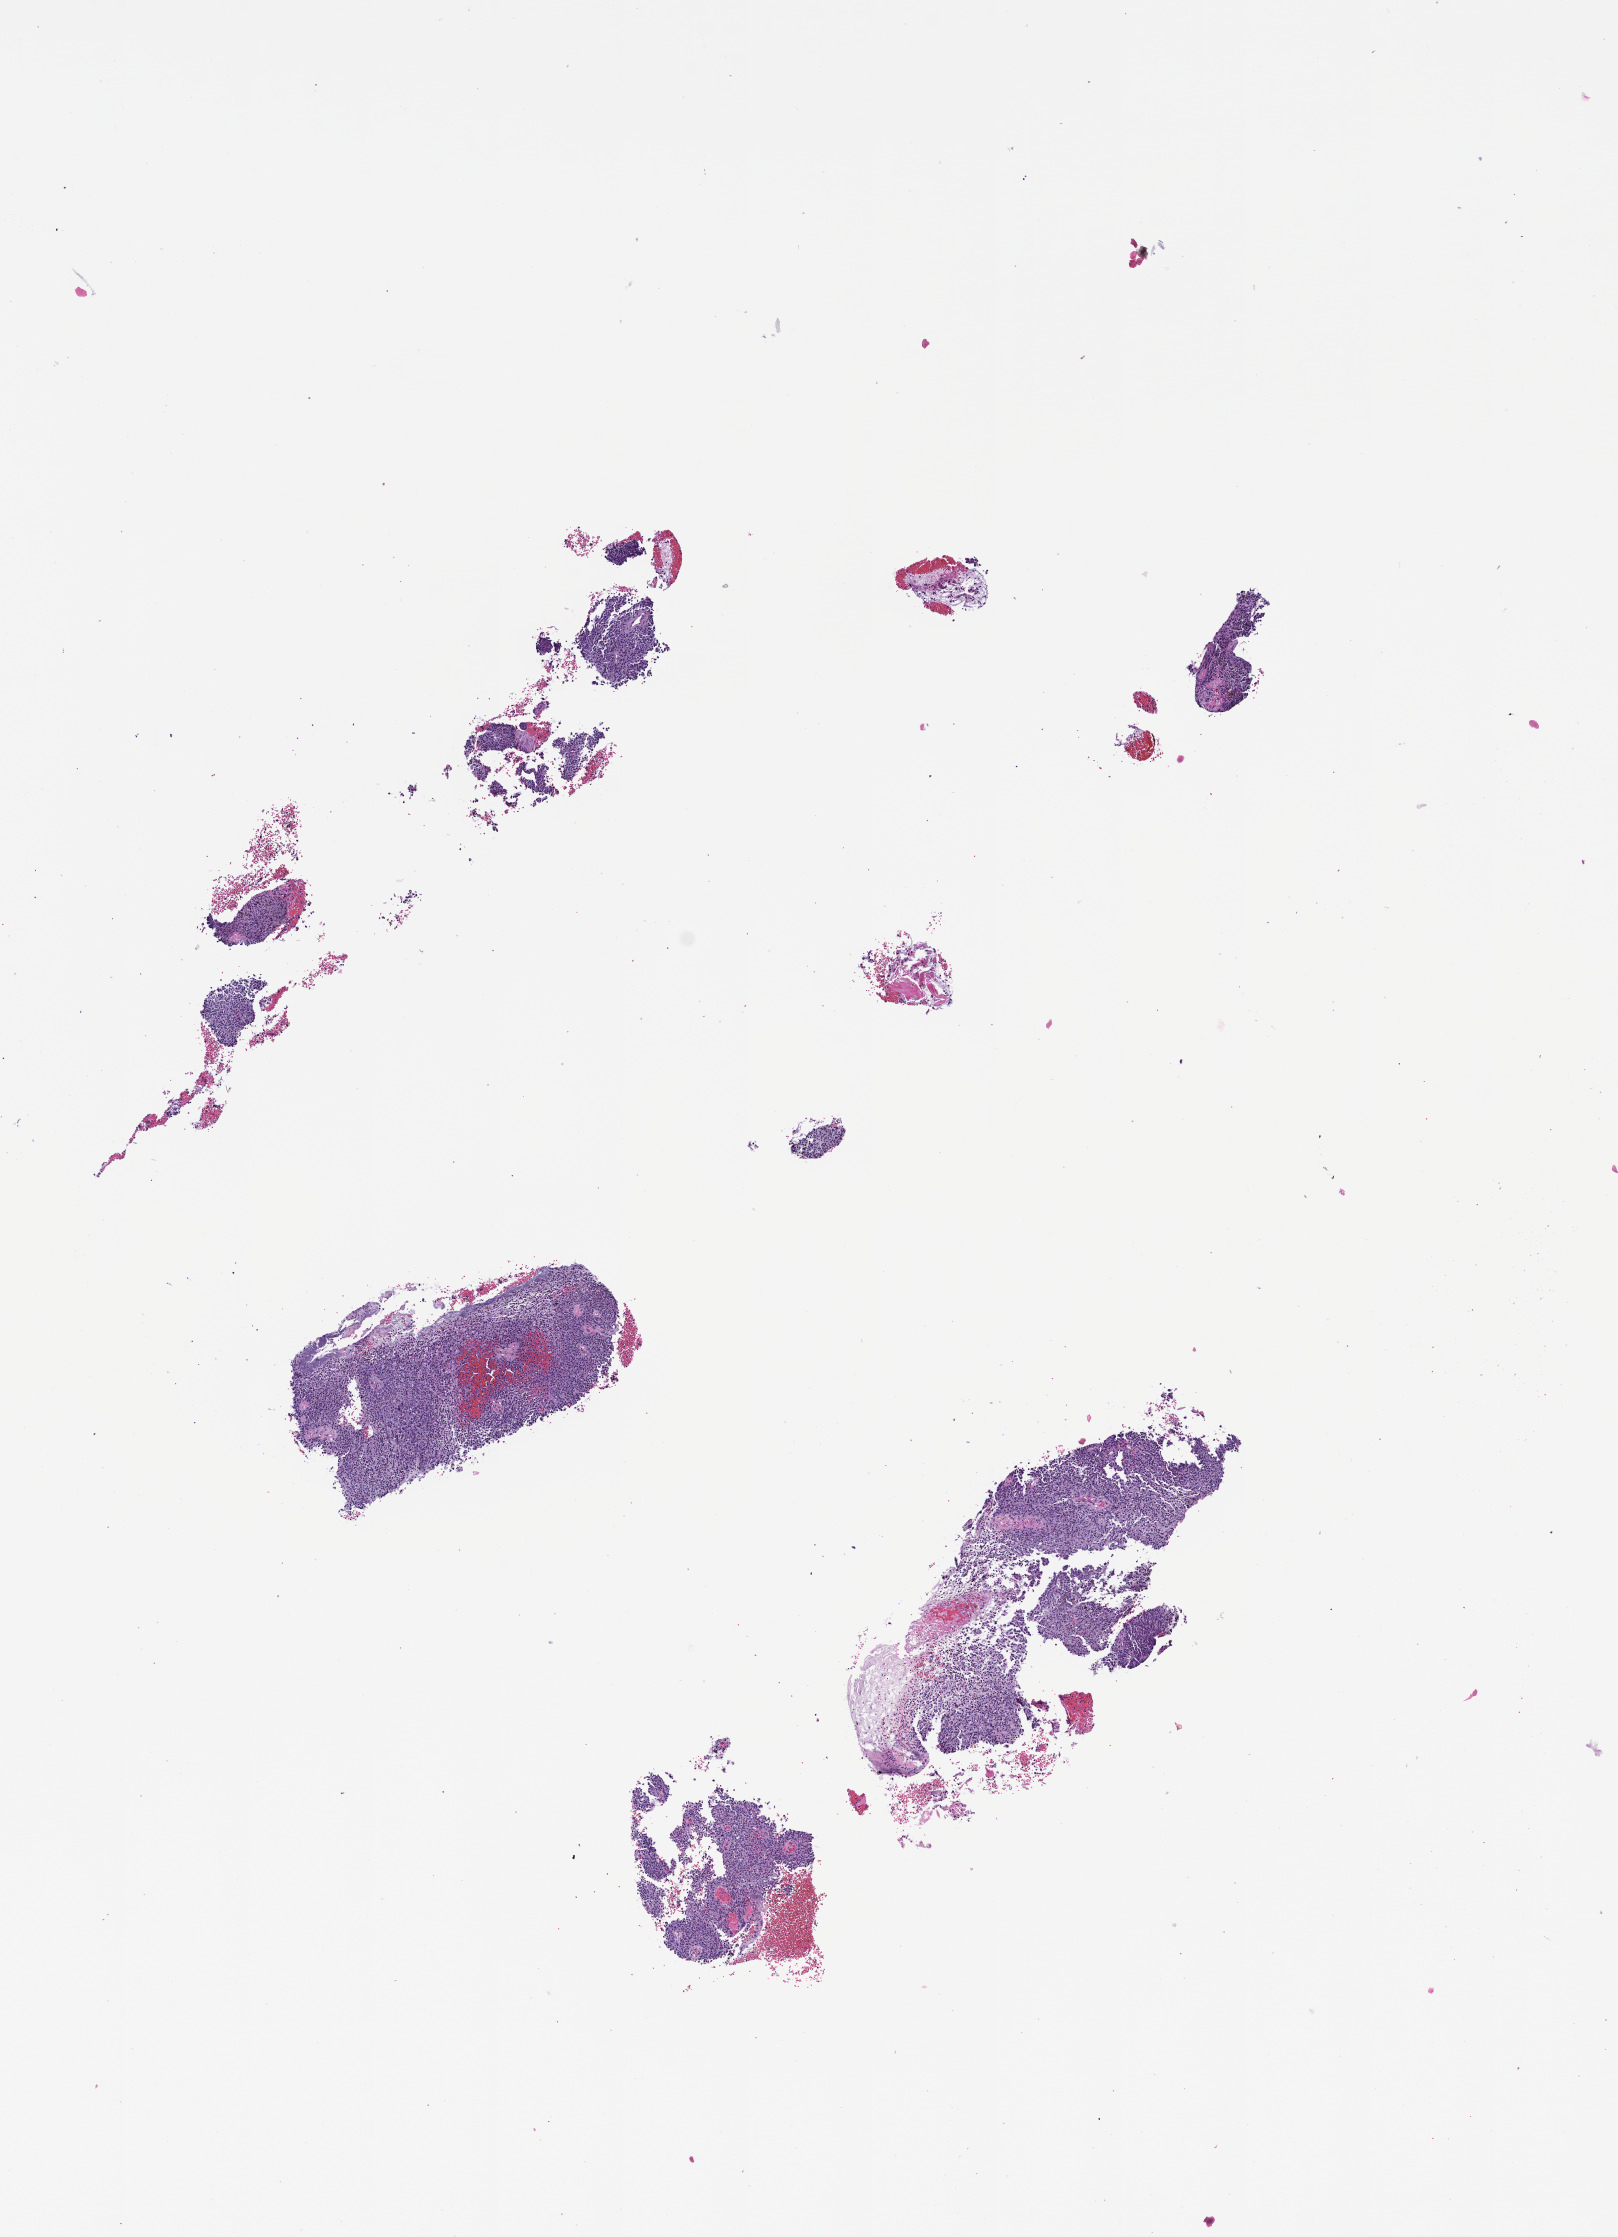
Whole-slide image, haematoxylin and eosin stain — low-resolution overview of the scanned area, about 6.5 x 9.0 mm, formalin-fixed, paraffin-embedded (FFPE) tissue, site: skin, specimen time point: archival tissue. Female patient.
• this section: primary tumor
• diagnosis: Melanoma